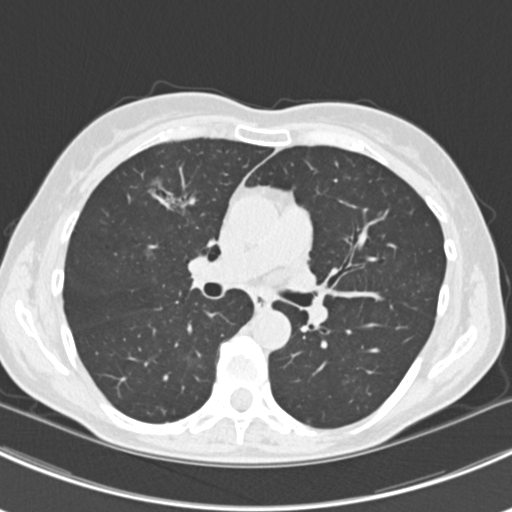
Axial slice from a low-dose chest CT screening exam. Baseline screening round. Lung window (W 1500 / L -600 HU). 2 mm slice thickness. Slice 80 of 224 in the series. 512 × 512 image matrix. Female, age 63 years at enrolment. Current smoker at enrolment.
• Lesion marked by an expert reader, bounding box [x1, y1, x2, y2] px = [144, 171, 201, 226].
• The screening reader recorded 10 non-calcified nodules or masses ≥4 mm on this exam; which of them this box marks is not recorded.
• Official screen result: positive, change unspecified: nodule(s) >= 4 mm or enlarging nodule(s), mass(es), or other non-specific abnormalities suspicious for lung cancer.
• Lung cancer was diagnosed 751 days after this screen (after the third annual screen): bronchiolo-alveolar adenocarcinoma, NOS, right upper lobe, right middle lobe, right lower lobe, left upper lobe, left lower lobe, moderately differentiated (G2), stage IV (AJCC 6th edition).